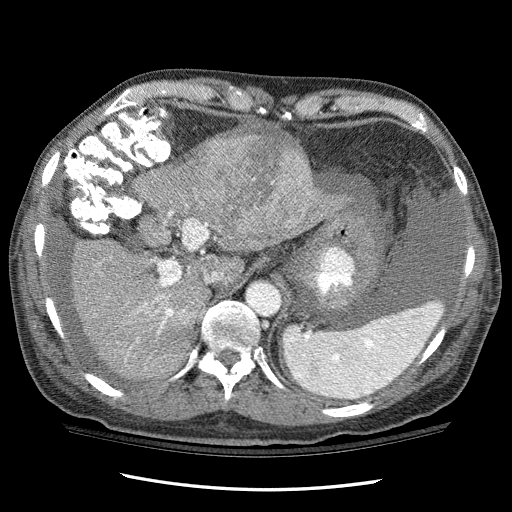
Contrast-enhanced abdominal CT (liver protocol), one axial slice. Slice 80 of 114 in the series (ordered by position). Reconstruction kernel STANDARD. One of 3 acquisitions stored at this slice position. Soft-tissue window (W 400 / L 40 HU). 2.5 mm slice thickness. 512 × 512 image matrix. Case-level facts recorded for this patient, not image findings: diagnosis: hepatocellular carcinoma (patient treated with transarterial chemoembolisation; whether this scan precedes or follows treatment is not stated here); TNM stage (as recorded): Stage-I; Child-Pugh class: C; tumour differentiation: well differentiated; tumour nodularity: uninodular.
Annotated regions visible in this slice (semi-automatic segmentation, software-assisted and operator-edited):
- abdominal aorta: bounding box [x1, y1, x2, y2] px = [247, 281, 280, 315]
- liver parenchyma outside the tumour (the mass and vessels are separate outlines, so this box may not span the whole liver): [69, 146, 336, 380]
- mass: [188, 125, 313, 241]
- liver vessels: [137, 272, 218, 341]